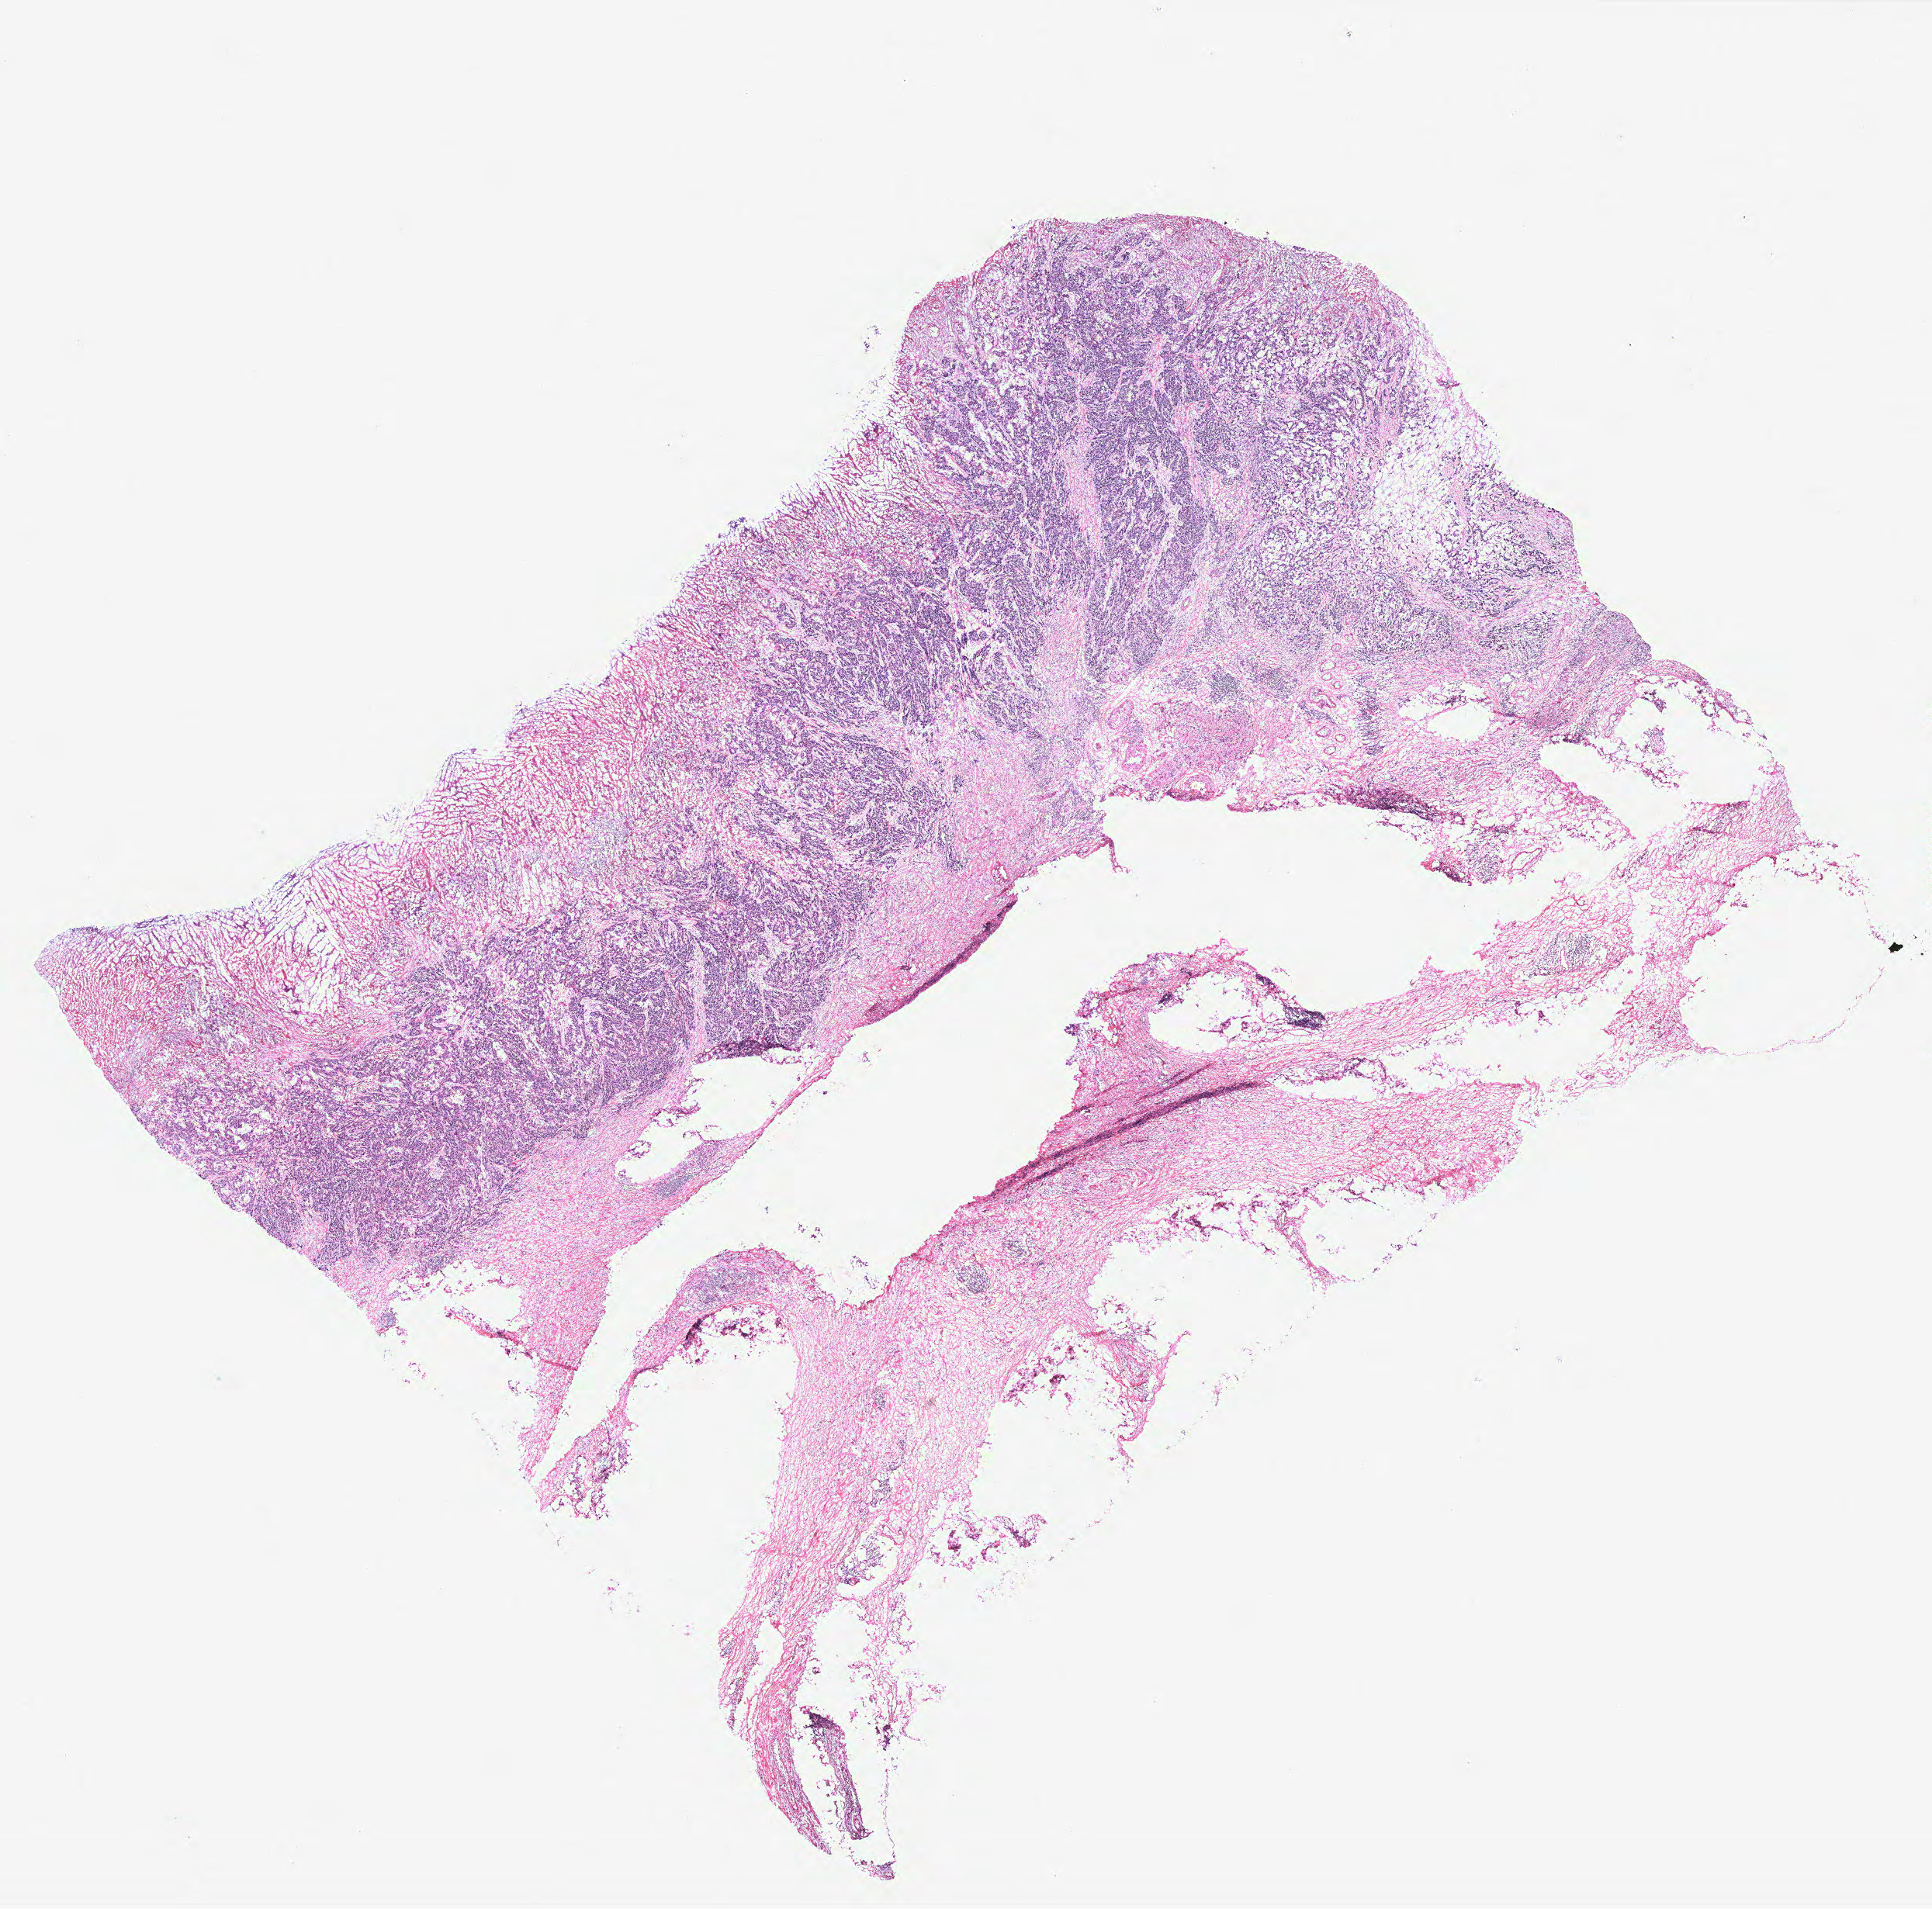
Digitized H&E-stained tissue section (whole slide), shown as a low-resolution overview of the whole scanned area (about 19.9 x 19.7 mm, acquisition: 40x scan), colon, tissue type not recorded.
* patient diagnosis (cohort enrolment): colon cancer (colon)